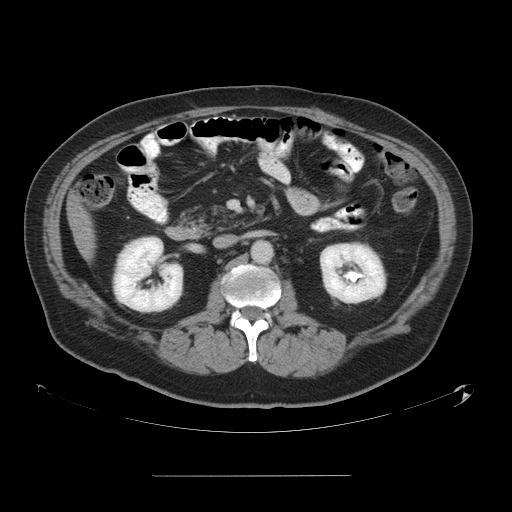
Contrast-enhanced abdominal CT, one axial slice. Position 20 of 58 along the scan axis. 120 kVp. Soft-tissue window (W 400 / L 40 HU). 512 × 512 image matrix, field of view 480 × 480 mm. Male patient, age 63 years. Case-level facts recorded for this patient, not image findings: diagnosis: colorectal cancer liver metastases, imaged before liver resection; multiple liver metastases: no; largest metastasis: 4.2 cm; disease in both lobes: no.
Structures marked on this image (manually delineated by an expert):
- liver: bounding box [x1, y1, x2, y2] px = [71, 199, 93, 256]
- planned liver remnant (the part of the liver to remain after resection): [71, 199, 93, 257]